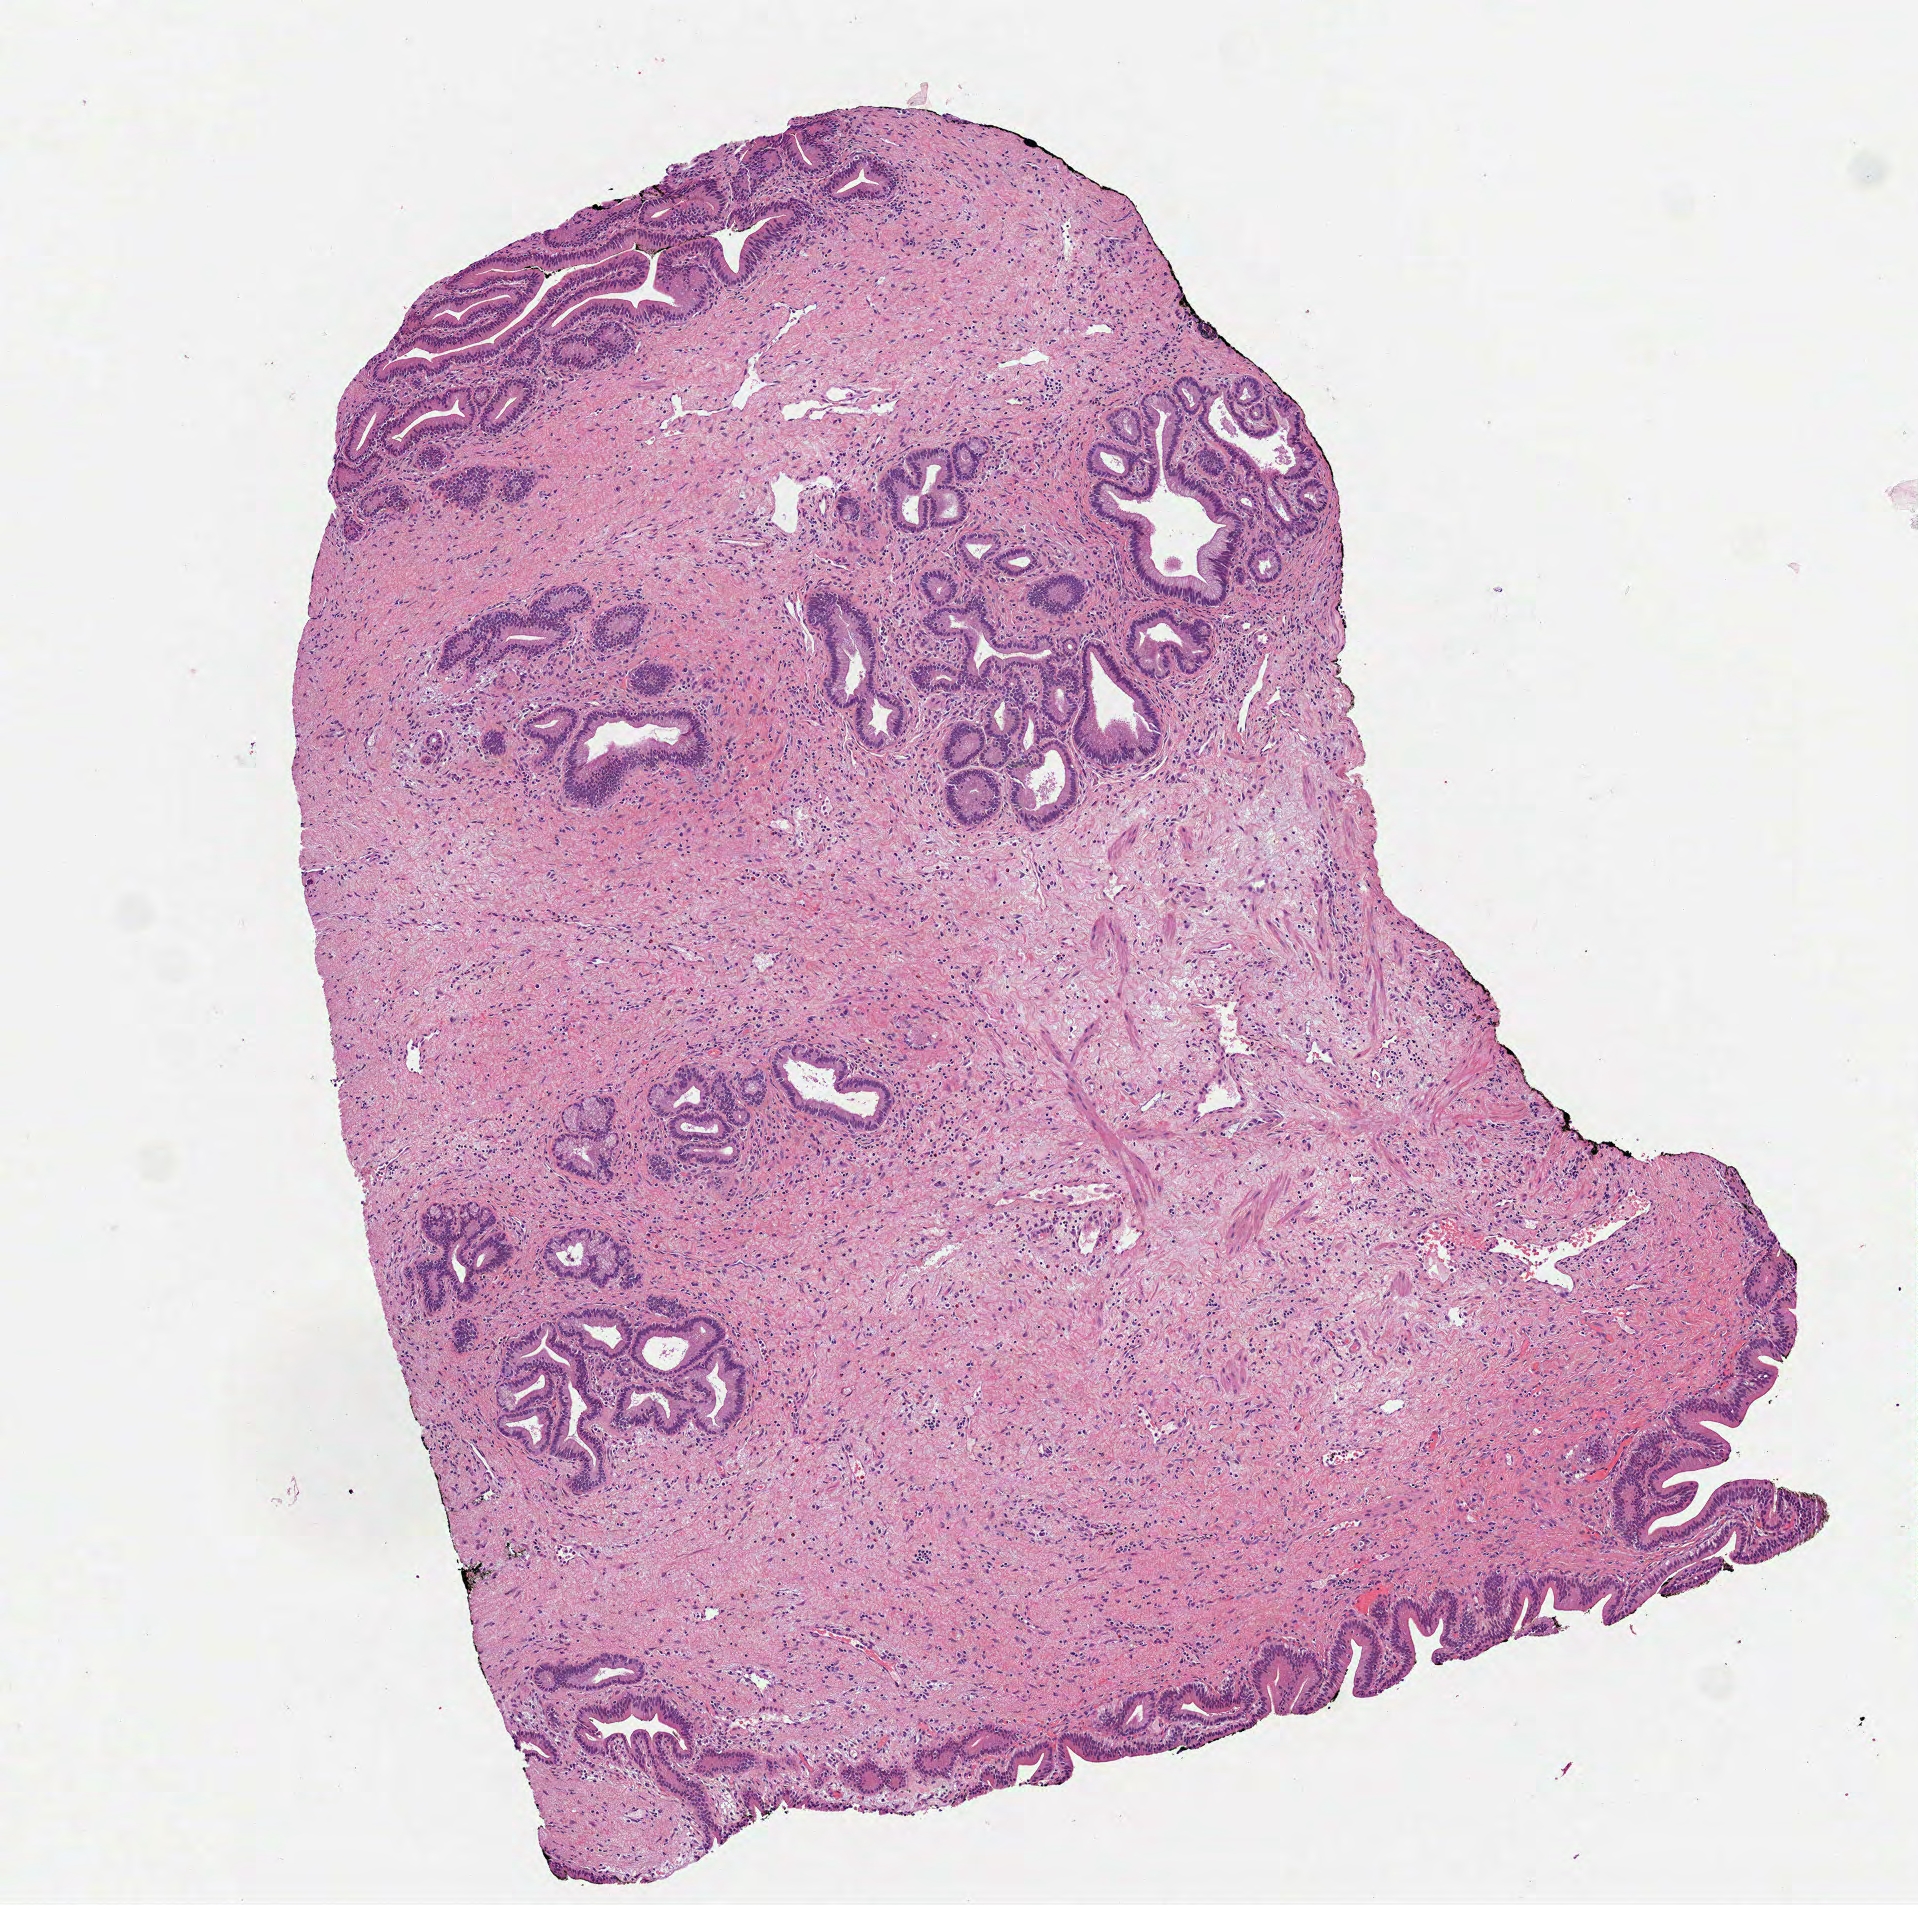
Digitized H&E-stained tissue section (whole slide) — a low-resolution overview of the entire scanned area, about 3.9 x 3.8 mm (acquisition: 40x scan), formalin-fixed paraffin-embedded (FFPE) diagnostic section, primary tumour sample from the pancreas. Male patient; age at initial diagnosis 57 years. Histologic grade: G1 (well differentiated).
• pathologic diagnosis: Infiltrating duct carcinoma, NOS (head of pancreas)
• AJCC pathologic stage: IIB
• lymph nodes positive (case pathology): 2 of 13 examined